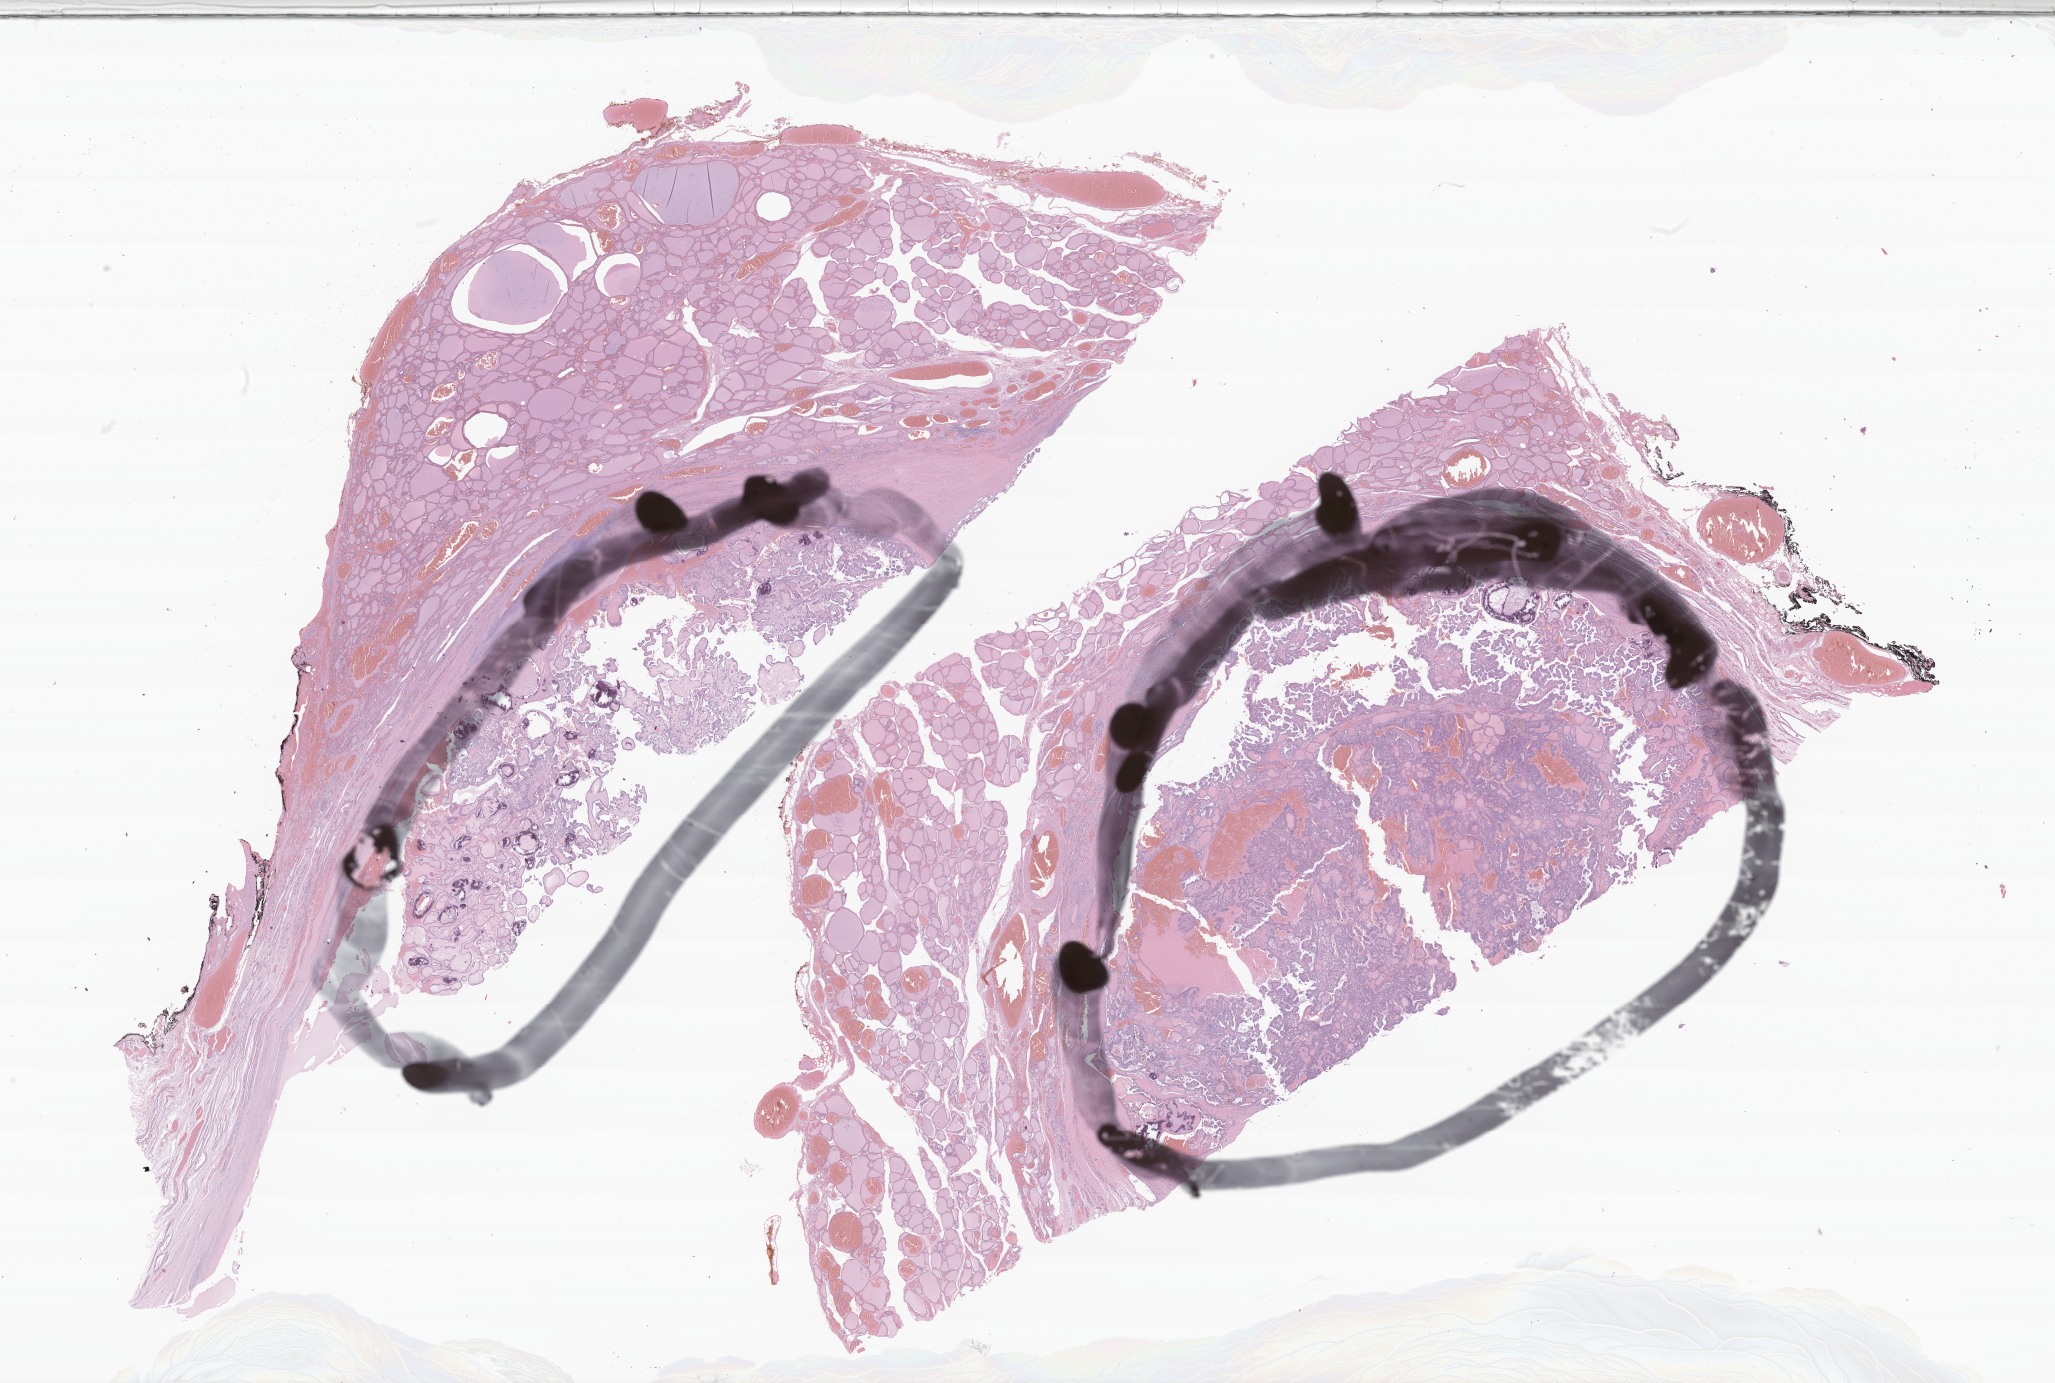
Digitized hematoxylin and eosin (H&E)-stained section of tumor tissue from the head and neck — shown as a low-resolution overview of the whole scanned area (about 34.6 x 23.3 mm), FFPE section. Patient: male, age 273 months.
- tissue or organ of origin (case record): head, face or neck
- diagnosis (ICD-O-3 morphology term): Papillary carcinoma, NOS